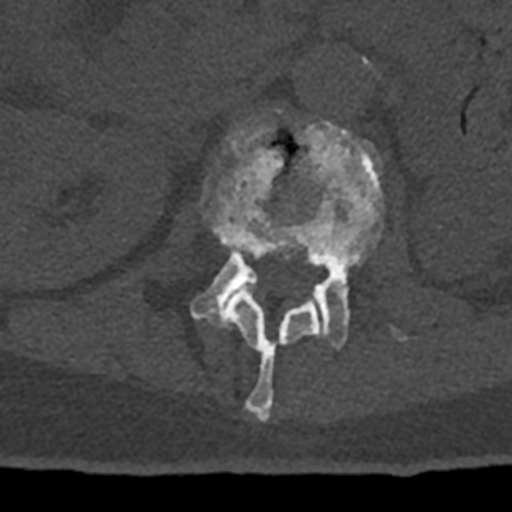
CT including the spine, one axial slice. Slice 405 of 797 in the series (ordered by position). Reconstruction kernel Br40s/3. Bone window (W 1800 / L 400 HU). 0.5 mm slice thickness. 512 × 512 image matrix, field of view 160 × 160 mm. Patient: male, 74 years. Case-level facts recorded for this patient, not image findings: primary cancer: renal.
Annotated regions visible in this slice (semi-automatically segmented with operator editing):
- L1 vertebra: bounding box <202,120,319,422> (left, top, right, bottom; pixels)
- L2 vertebra: <190,122,406,349>